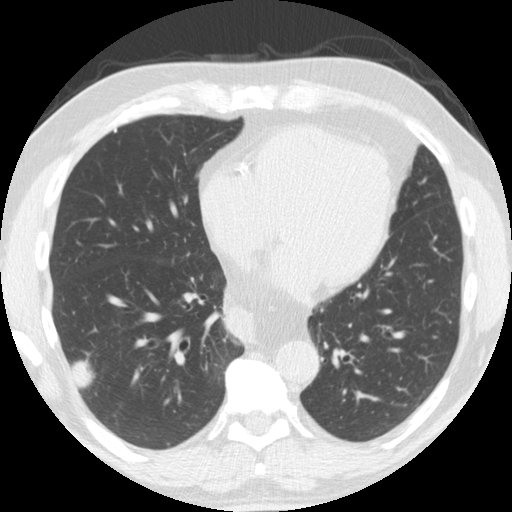
Axial slice from a low-dose chest CT screening exam; second screening round (one year after baseline); lung window (W 1500 / L -600 HU); 2.5 mm slice thickness; slice 106 of 174 in the series. Male, age 61 years at enrolment. Former smoker at enrolment.
Lesion marked by an expert reader, bounding box [x1, y1, x2, y2] px = [43, 320, 111, 397]. Screening reader's record for this exam (one nodule recorded; not confirmed to be the boxed lesion): non-calcified nodule or mass ≥4 mm, right lower lobe, 33 × 19 mm, smooth margins, soft tissue attenuation, pre-existing on the prior screen: yes; interval growth: yes. Later outcome: lung cancer diagnosed 30 days after this screen — adenosquamous carcinoma, right lower lobe, poorly differentiated (G3), stage IV (AJCC 6th edition), 45 mm at pathology.